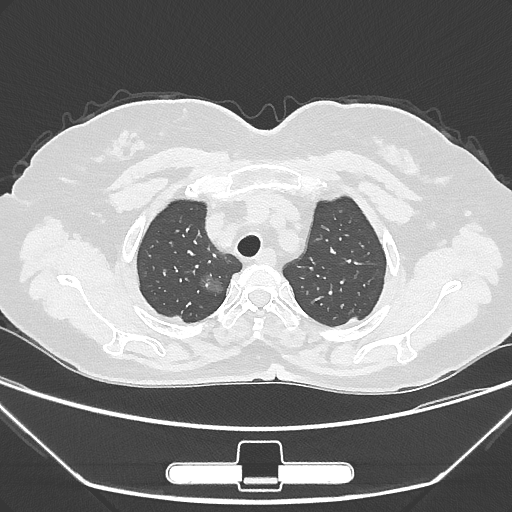
Chest CT, one axial slice; position 233 of 275 along the scan axis; reconstruction kernel IMR1,SharpPlus; lung window (W 1500 / L -600 HU); 1 mm slice thickness; 512 × 512 image matrix, field of view 356 × 356 mm. Female patient, age 63 years. From the clinical record (not read from this slice): clinical TNM (as recorded): T1a N0 M0; histopathological grade: G1.
Structures marked on this image (rectangle marked by the reading radiologist):
- lung tumour (recorded histology: adenocarcinoma): bounding box (x1, y1, x2, y2) in pixels: (191, 265, 225, 301)